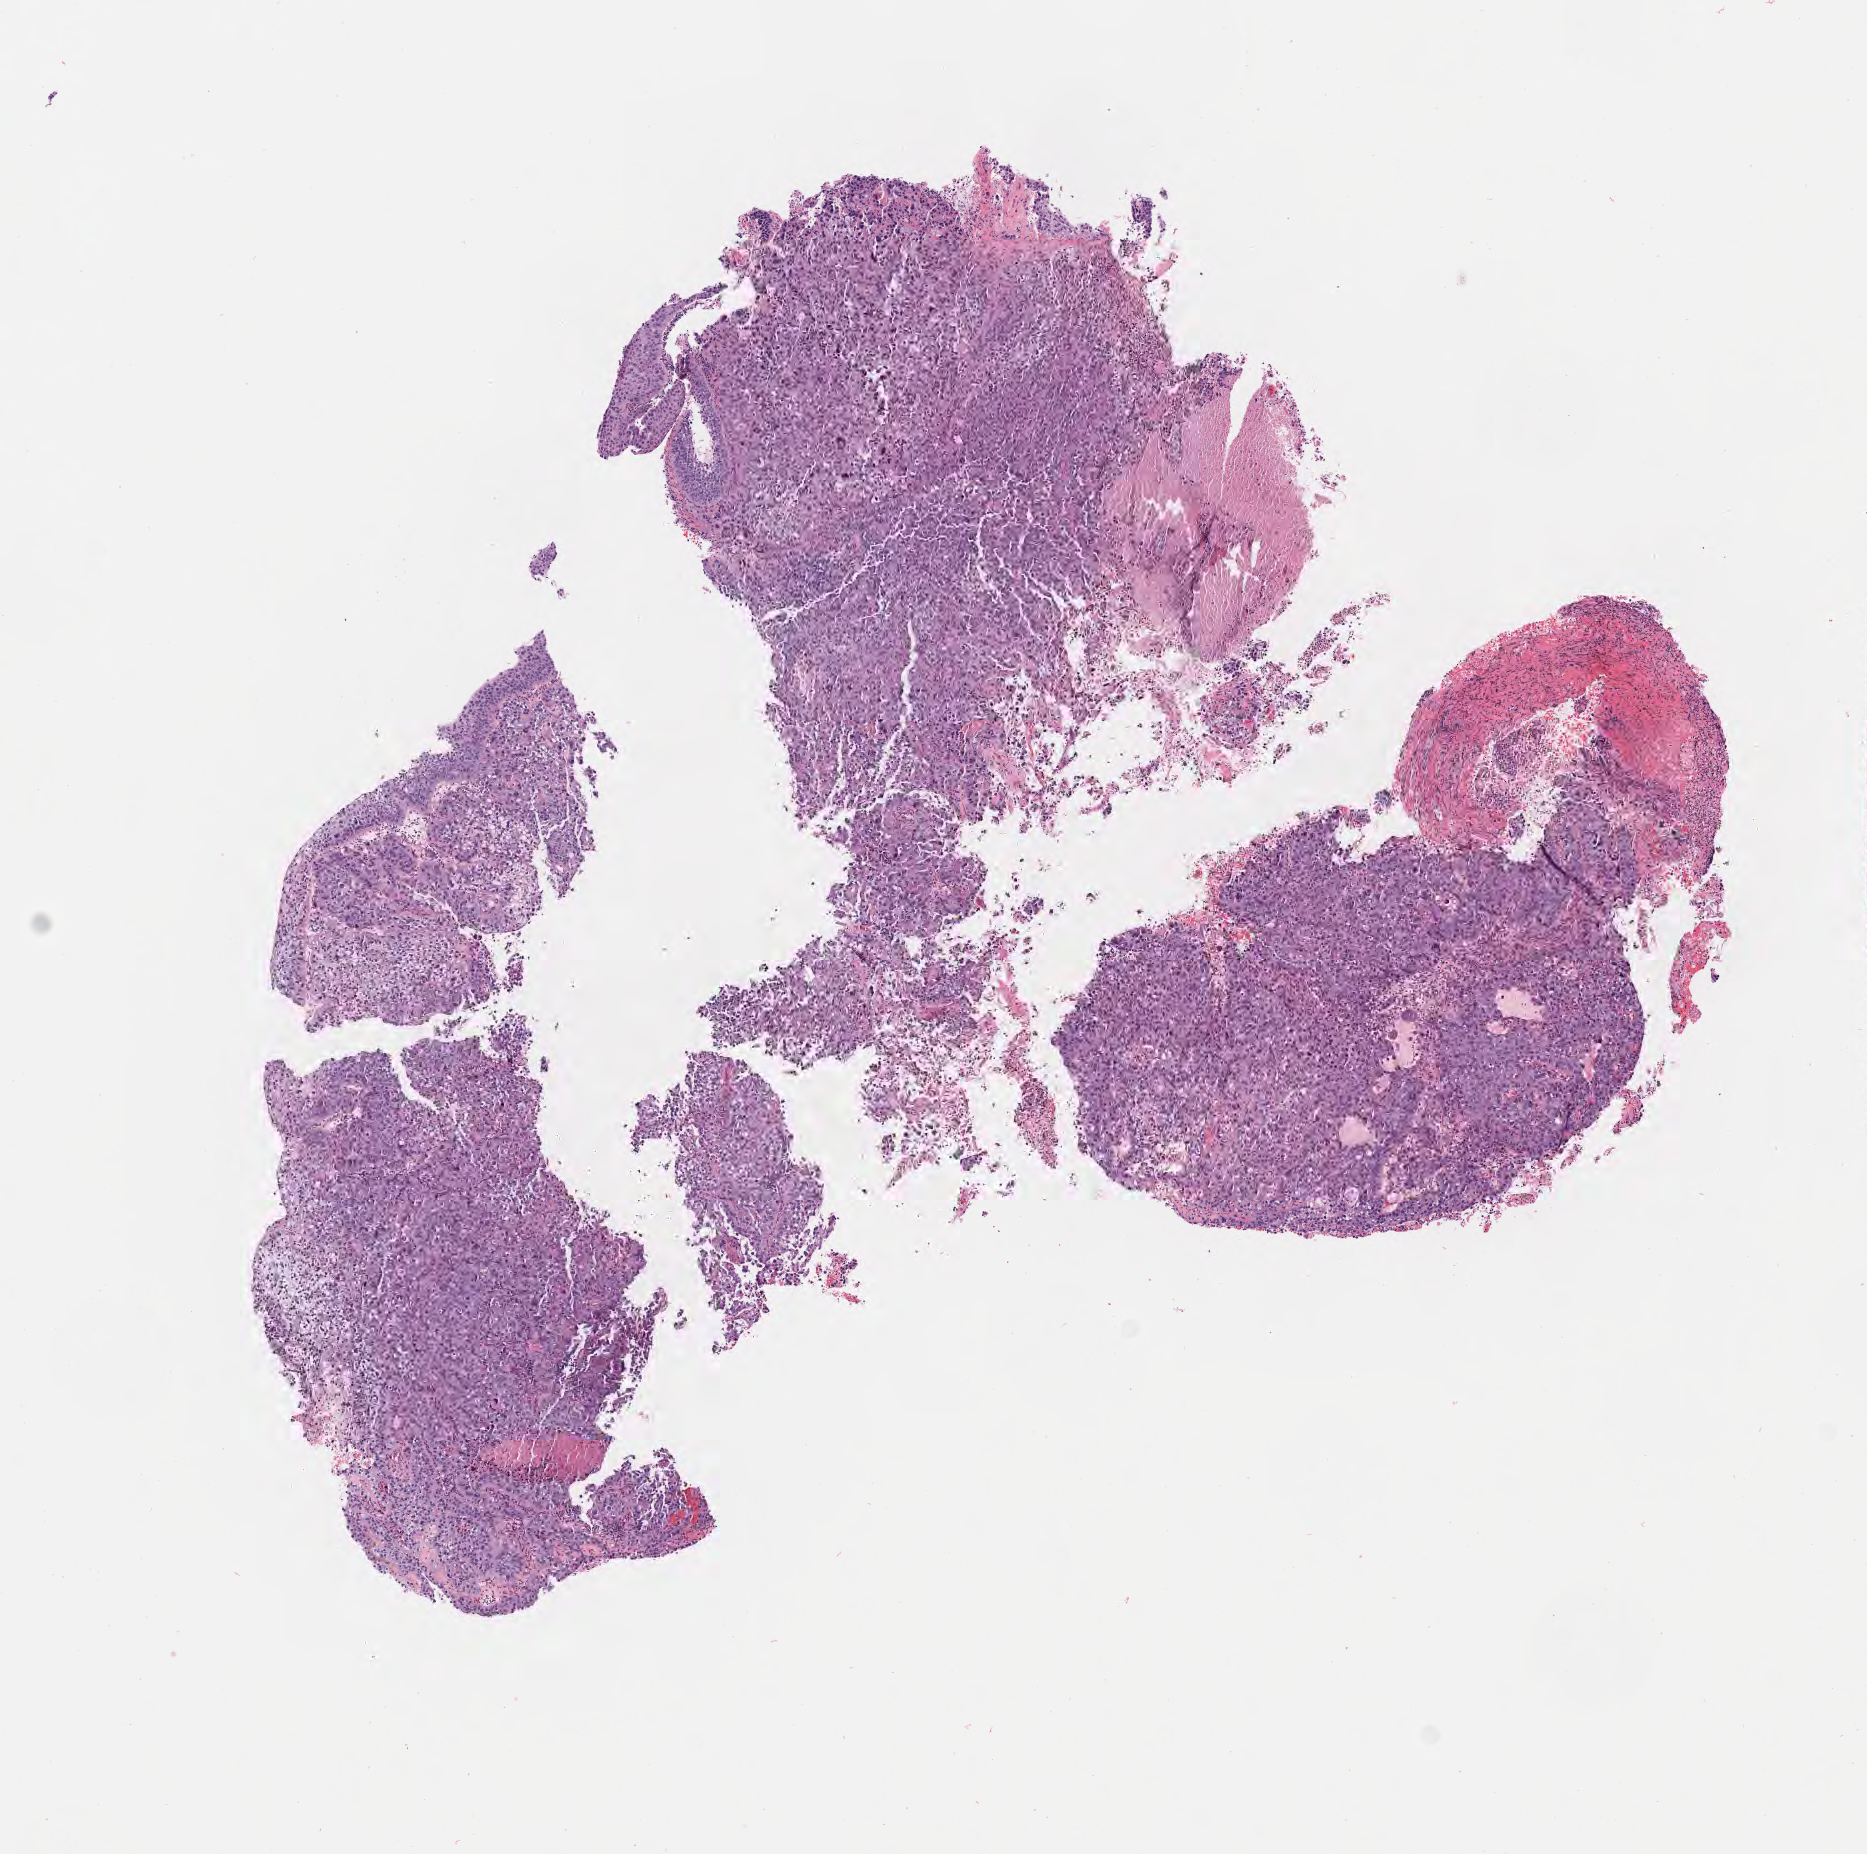
Hematoxylin and eosin (H&E) whole-slide image — shown as a low-resolution overview of the whole scanned area (about 7.6 x 7.5 mm), specimen: tumor tissue, anatomic site: cervix. Patient female; 56 years old.
Histologic diagnosis: Adenocarcinoma, NOS.